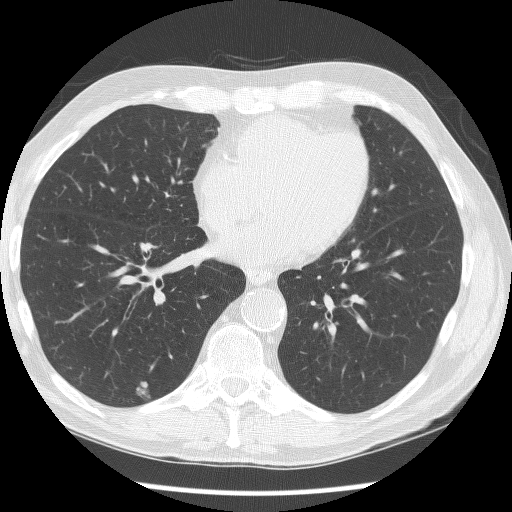
Chest CT (low-dose screening protocol), one axial image. Baseline screening round. Lung window (W 1500 / L -600 HU). Lung (sharp) reconstruction kernel (BONE). Slice 107 of 190 in the series. 512 × 512 image matrix. Male participant, aged 62 years at enrolment. Current smoker at enrolment.
• Expert-annotated lung lesion, bounding box <126,376,166,413> (left, top, right, bottom; pixels).
• The screening reader recorded 2 non-calcified nodules or masses ≥4 mm on this exam (right lower lobe, right lower lobe); which of them this box marks is not recorded.
• Participant outcome: lung cancer diagnosed 849 days after this screen — adenocarcinoma, NOS, right lower lobe, moderately differentiated (G2), stage IIIB (AJCC 6th edition), 15 mm at pathology.